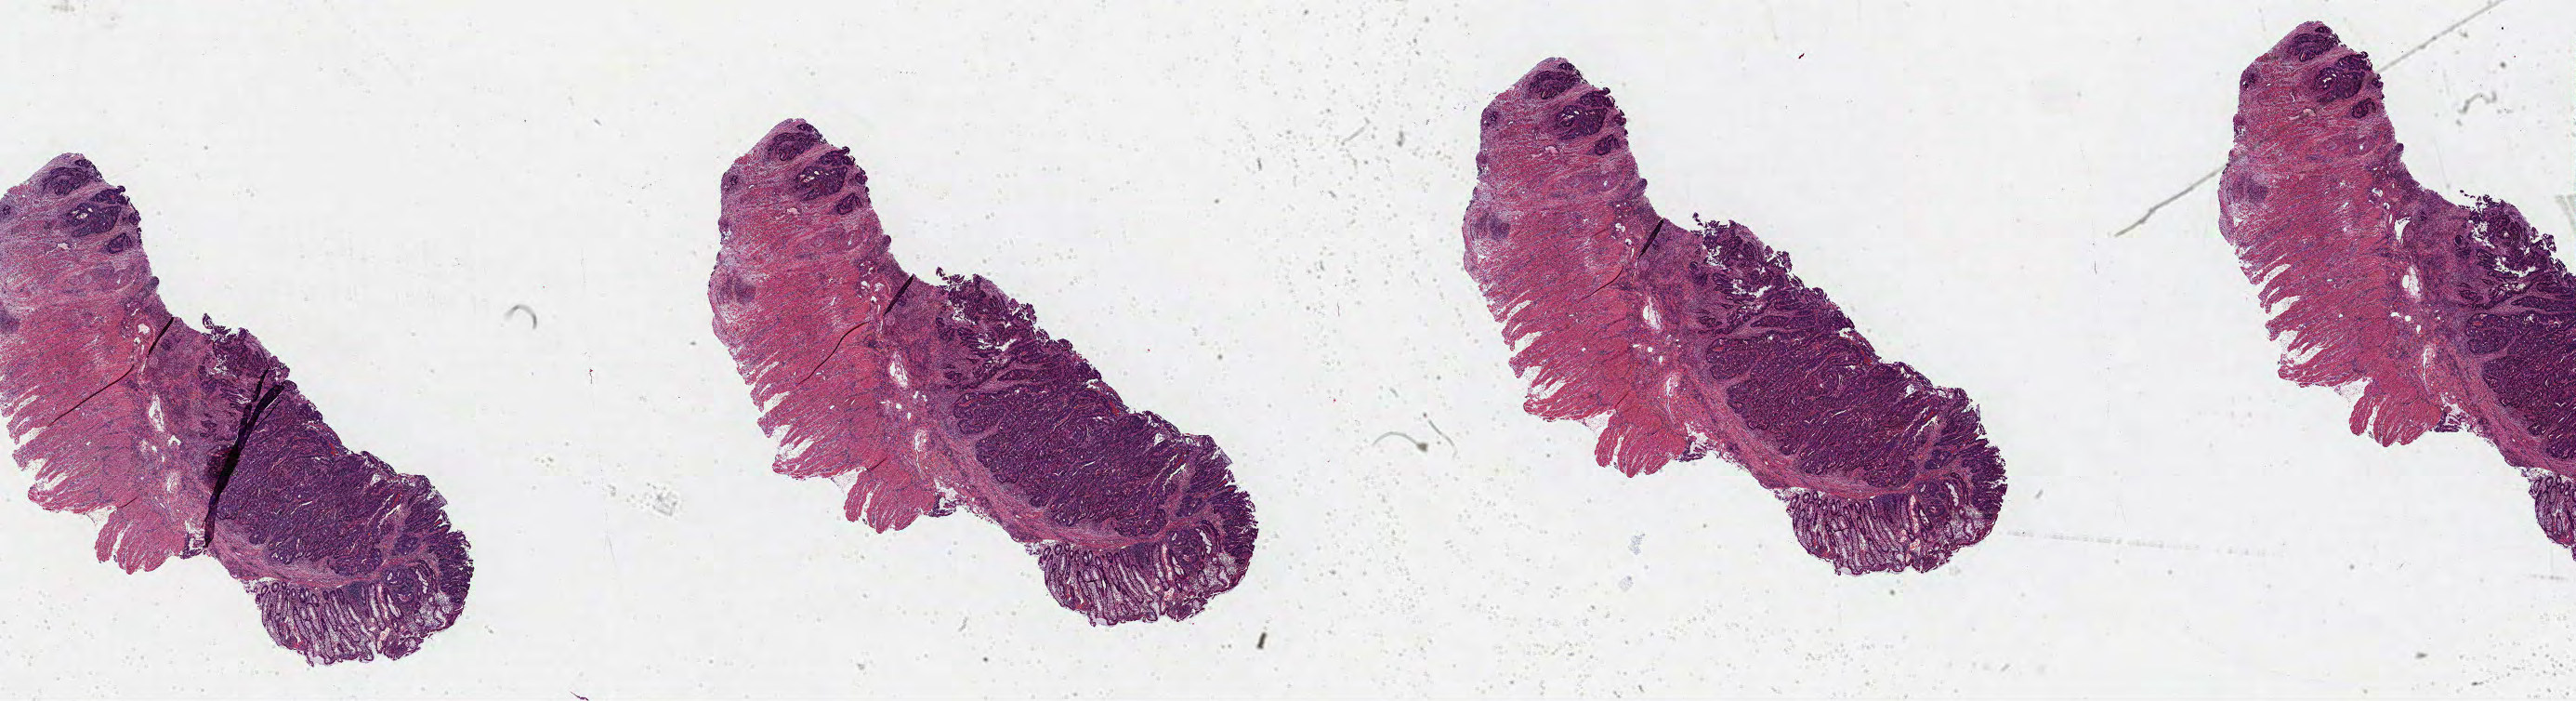
H&E-stained whole-slide image, low-resolution overview of the scanned area, about 44.7 x 12.2 mm; formalin-fixed paraffin-embedded (FFPE) diagnostic section; sample: primary tumour, colon. Patient: male, age at initial diagnosis 79 years.
TNM: T3 N0 M0. Histologic diagnosis: Adenocarcinoma, NOS (ascending colon). AJCC pathologic stage: IIA (7th edition). Lymph nodes positive (case pathology): 0 of 19 examined.